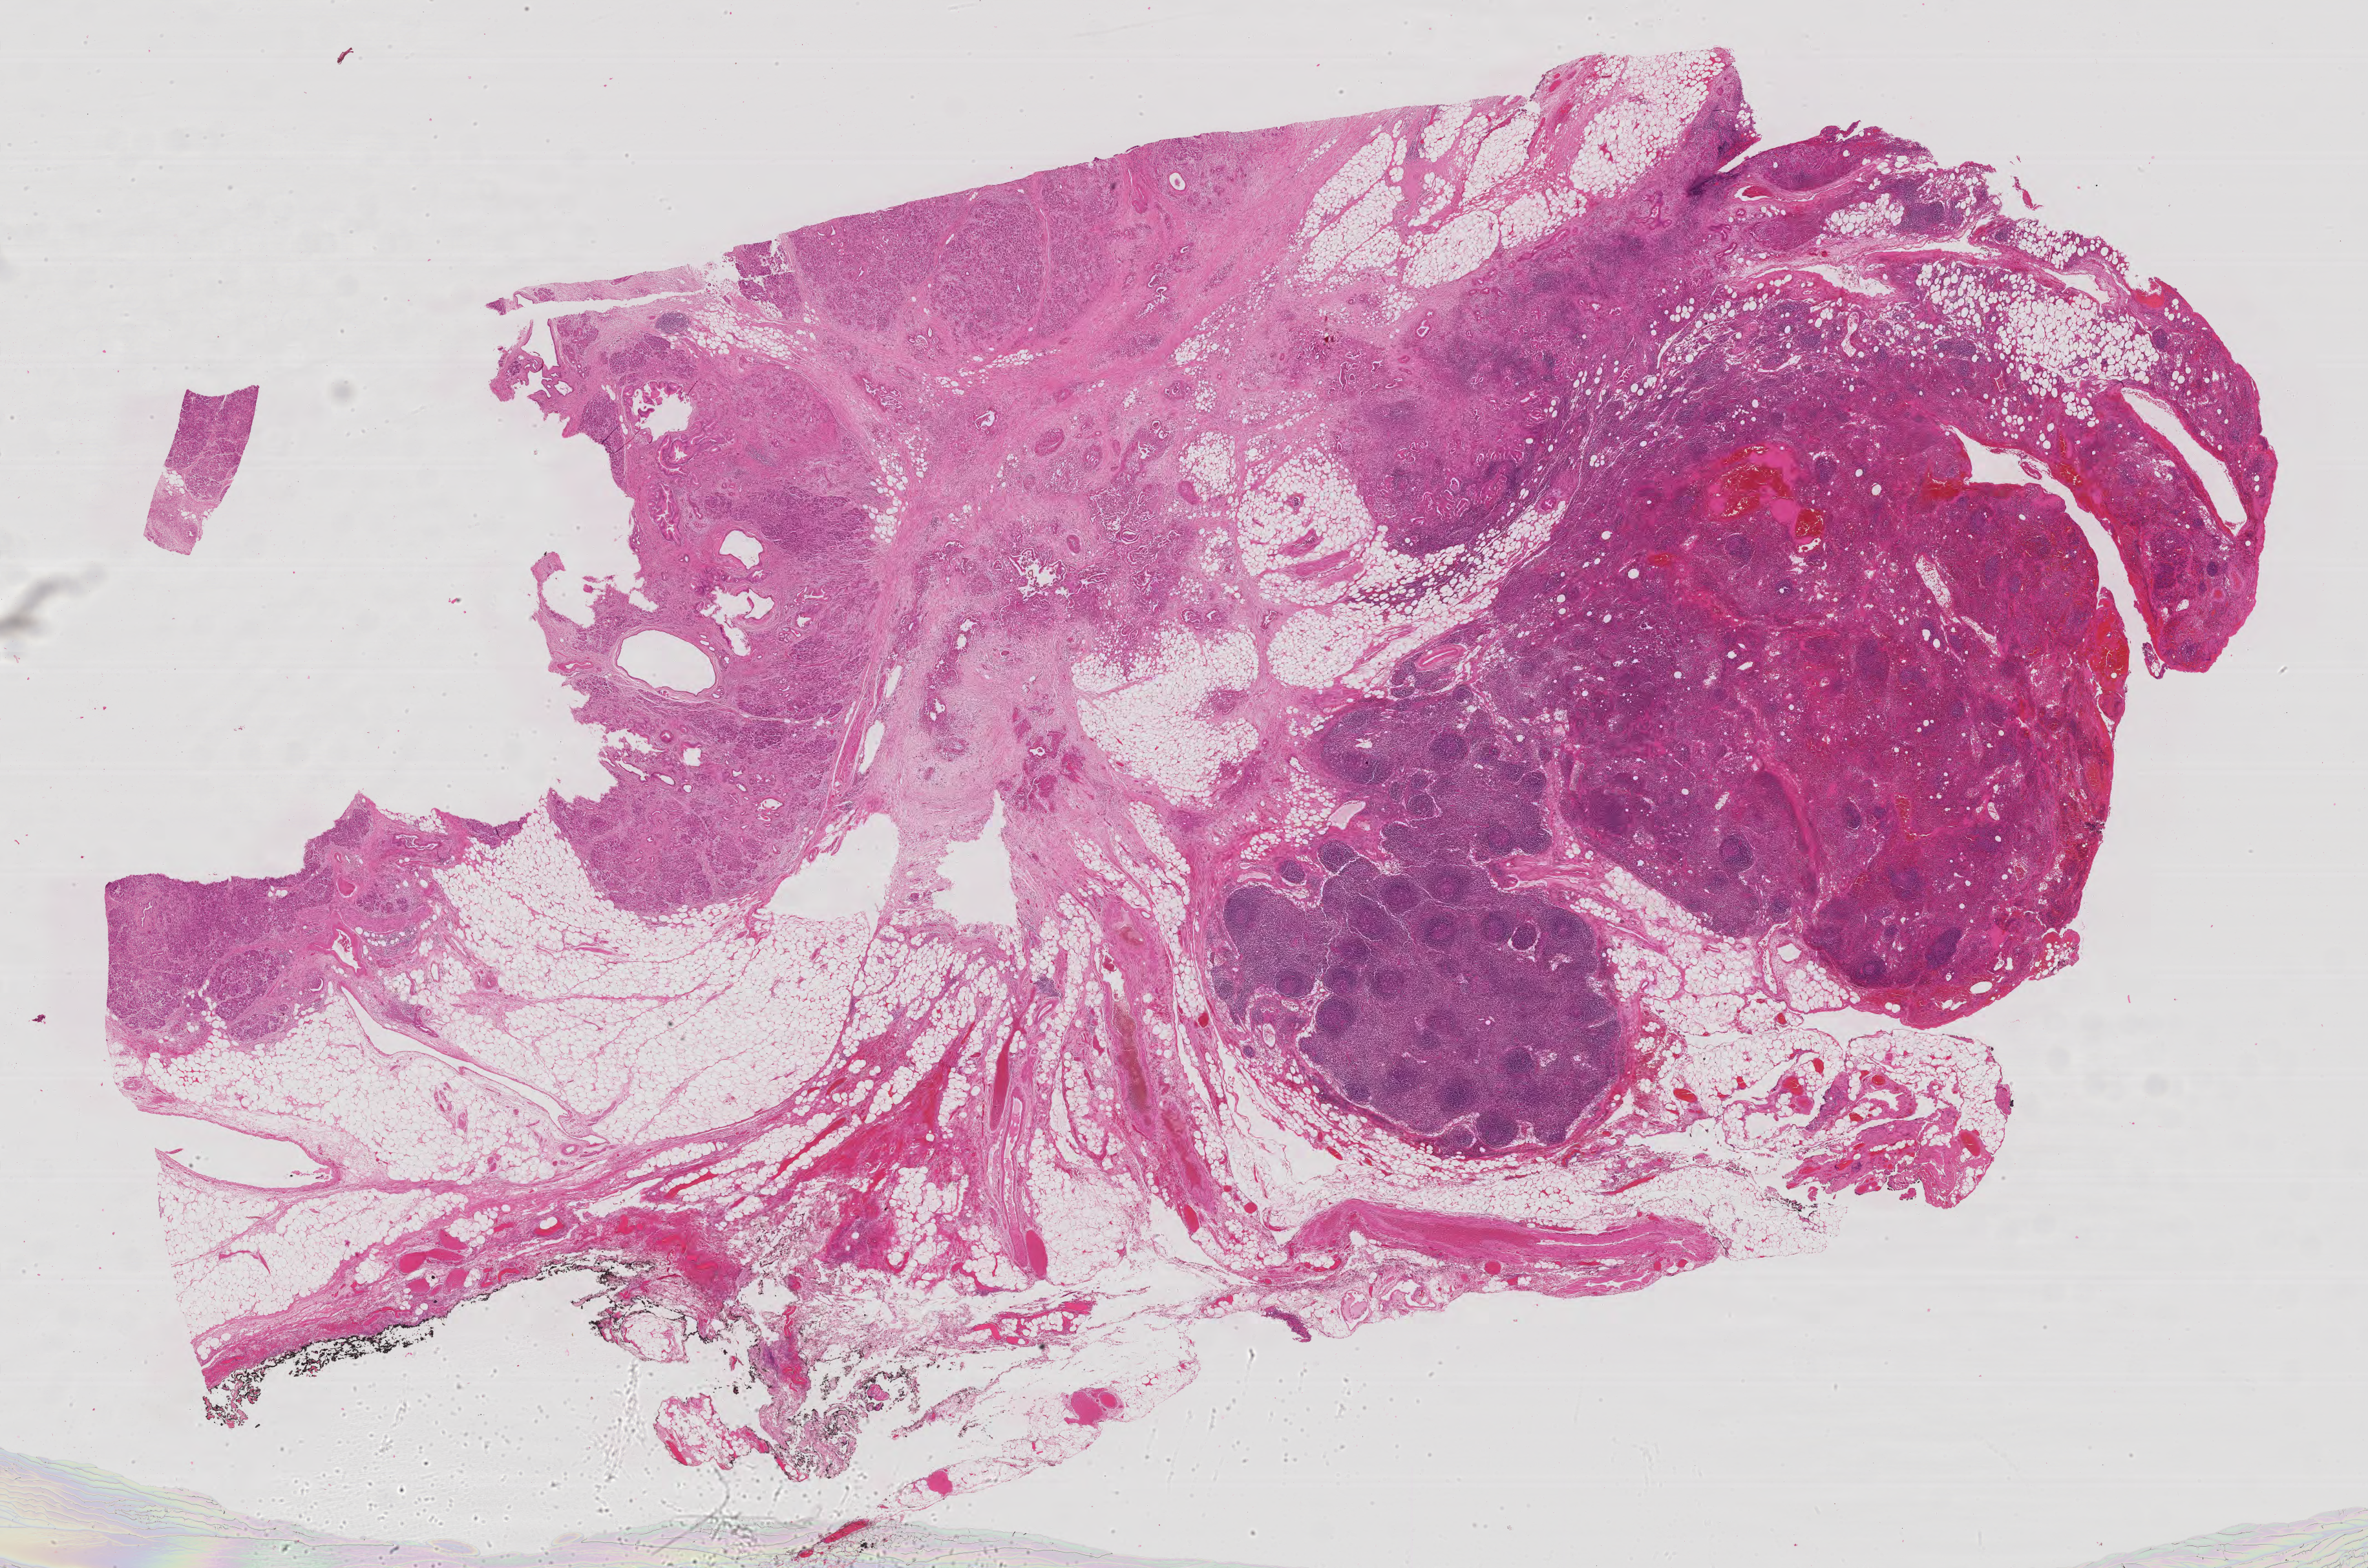
H&E-stained whole-slide image, low-resolution overview of the scanned area, about 29.3 x 19.4 mm; FFPE section; sample: primary tumour, pancreas. Patient: male, age at initial diagnosis 67 years. Histologic grade: G3 (poorly differentiated).
AJCC pathologic stage: IIB (6th edition). Pathologic diagnosis: Infiltrating duct carcinoma, NOS (body of pancreas).